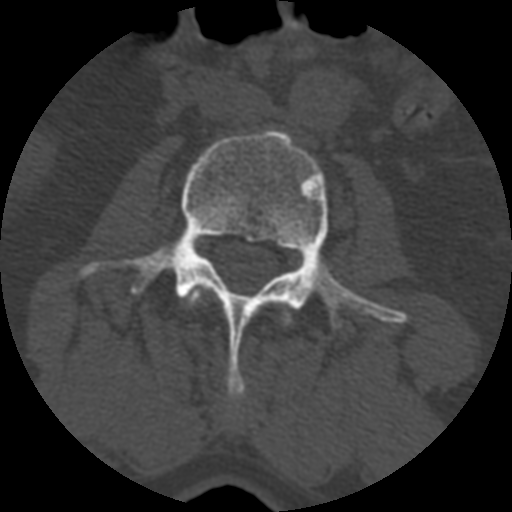
CT including the spine, one axial slice; position 308 of 399 along the scan axis; bone window (W 1800 / L 400 HU); 1.25 mm slice thickness; 512 × 512 image matrix, field of view 160 × 160 mm. Patient age 71 years. Case-level facts recorded for this patient, not image findings: primary cancer: prostate.
Annotated regions visible in this slice (semi-automatically segmented with operator editing):
- L2 vertebra: bounding box [x1, y1, x2, y2] px = [187, 290, 290, 326]
- L3 vertebra: [80, 131, 406, 402]